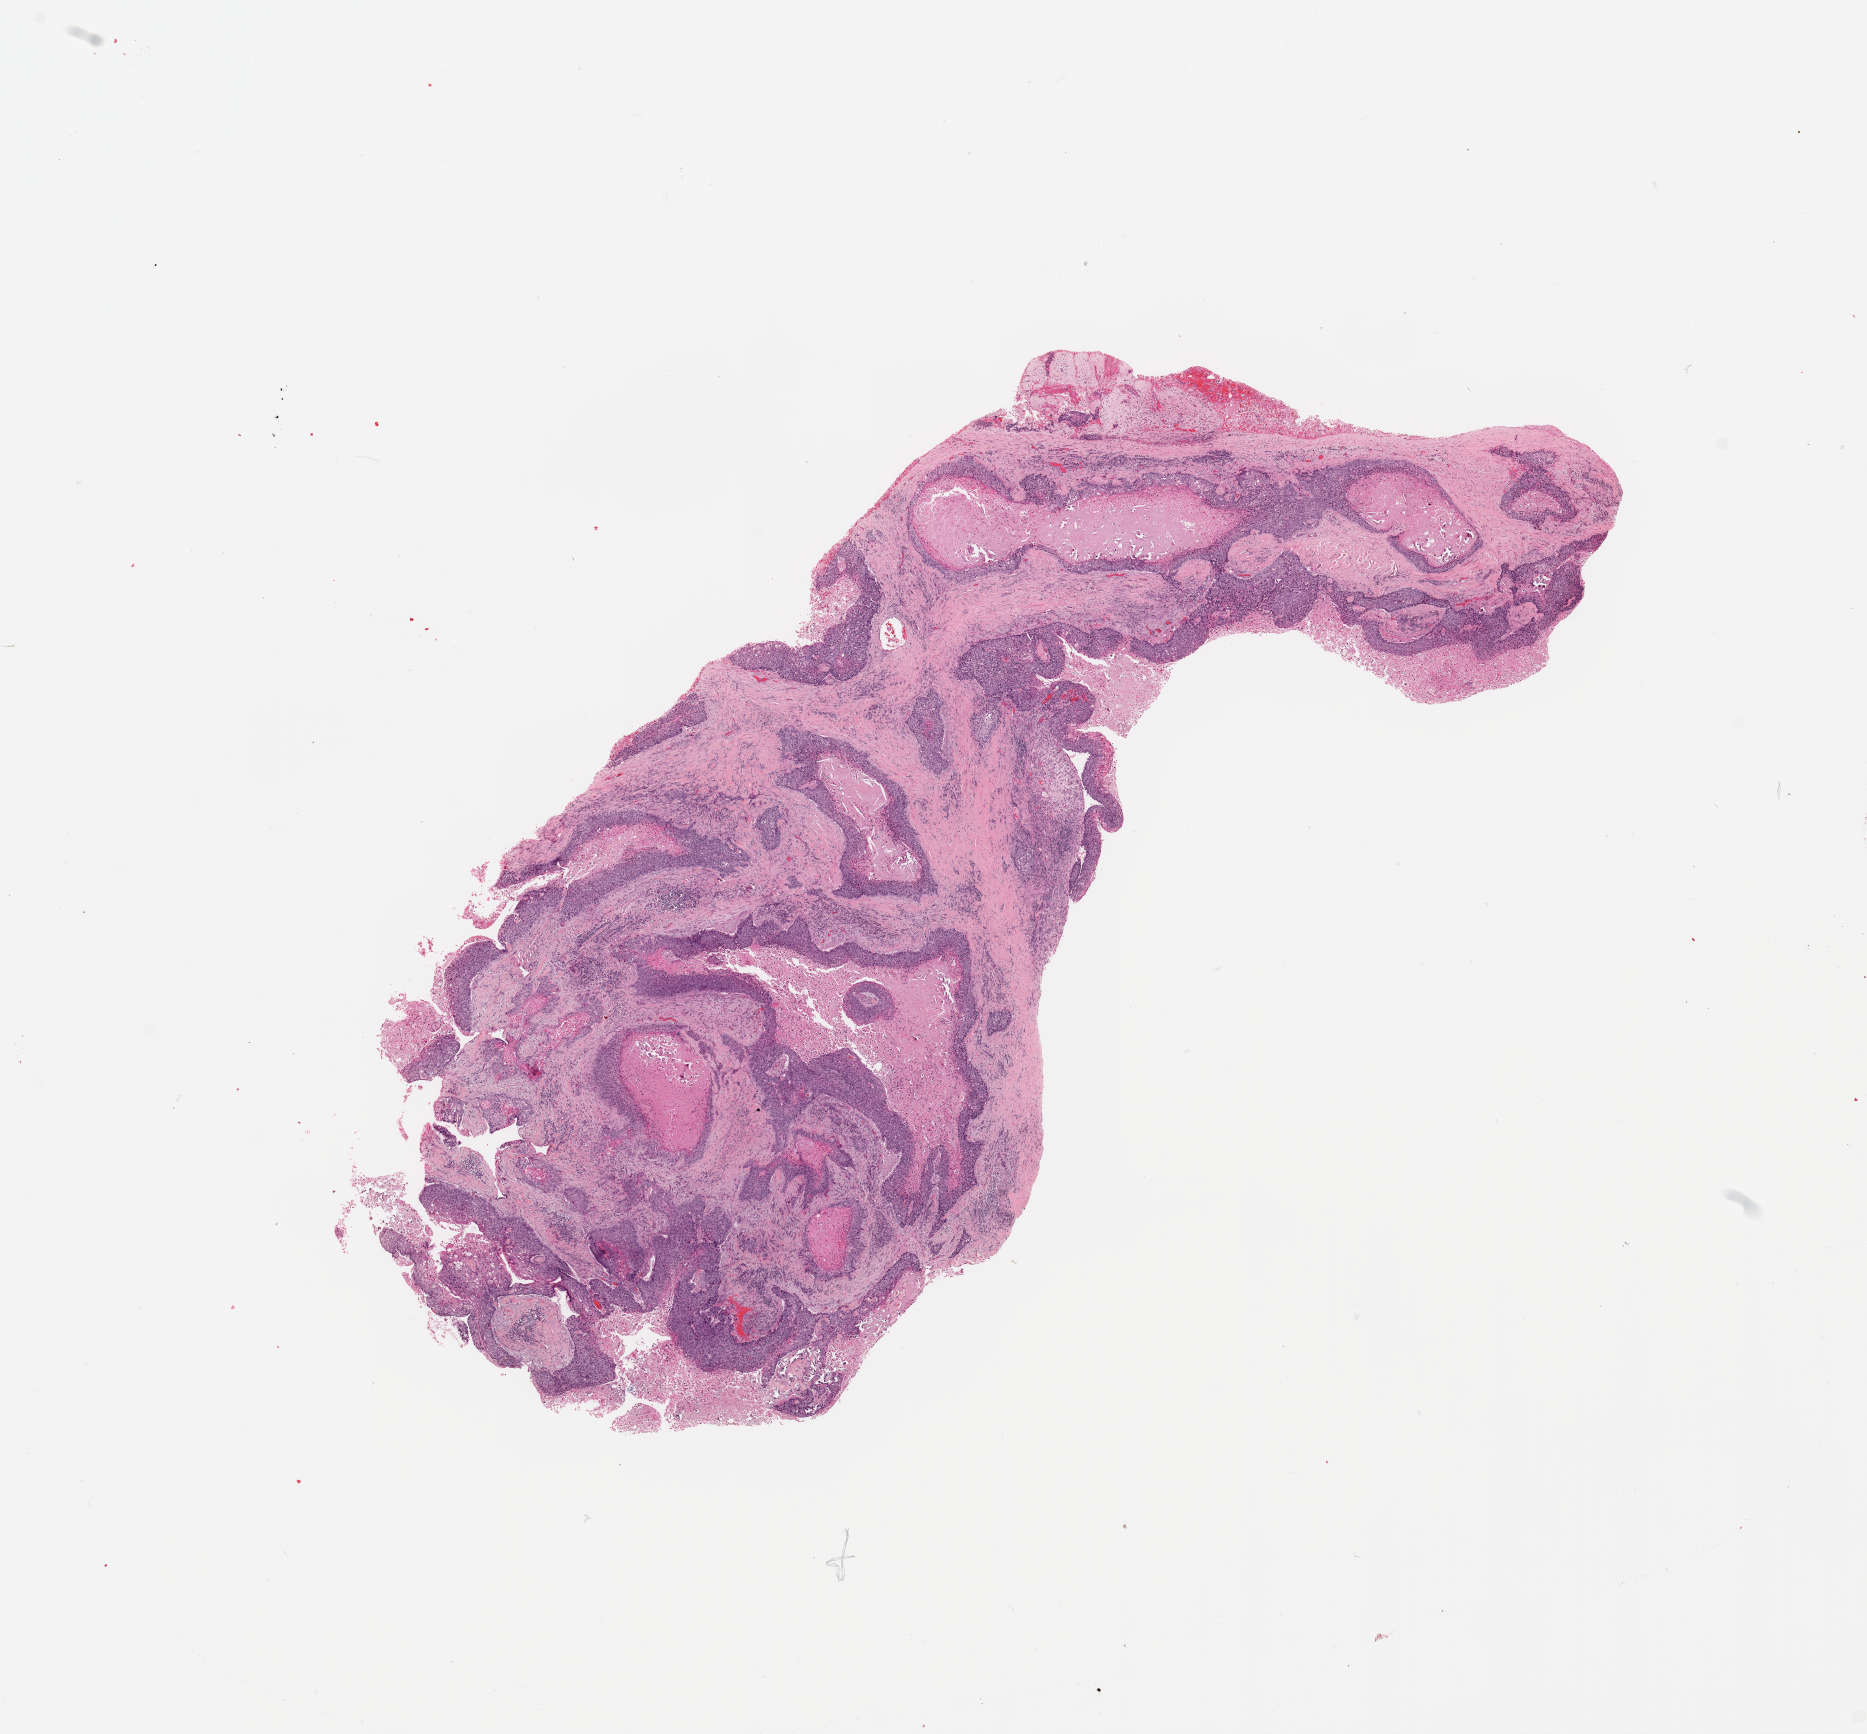
Digitized H&E-stained tissue section (whole slide) — low-resolution overview of the scanned area, about 14.8 x 13.7 mm (from a 20x scan); tumour tissue sample, sampled site: lung. 78-year-old male patient. Histologic grade: G2 (moderately differentiated). Composition of this section per pathologist review: tumour nuclei 60%, necrosis 20%.
- histologic diagnosis: Squamous cell carcinoma, NOS
- primary tumour site (as recorded): right middle lobe
- AJCC pathologic stage: III